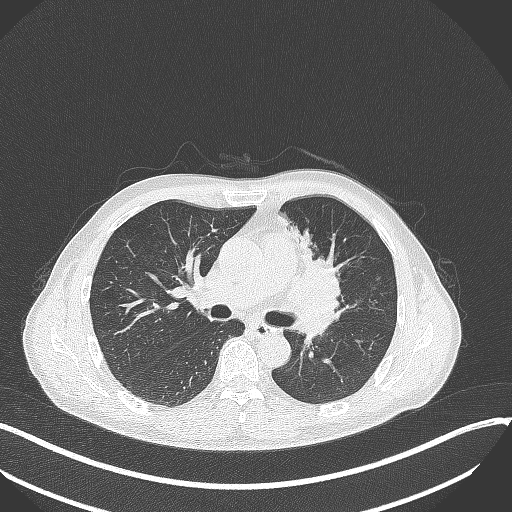
Chest CT, one axial slice; position 198 of 411 along the scan axis; 120 kVp; lung window (W 1500 / L -600 HU); 512 × 512 image matrix. Male patient, age 56 years. Case-level facts recorded for this patient, not image findings: clinical TNM (as recorded): T2a N0 M0.
Outlined on this slice (rectangle marked by the reading radiologist):
- lung tumour (recorded histology: squamous cell carcinoma): bounding box [x1, y1, x2, y2] px = [287, 239, 355, 315]